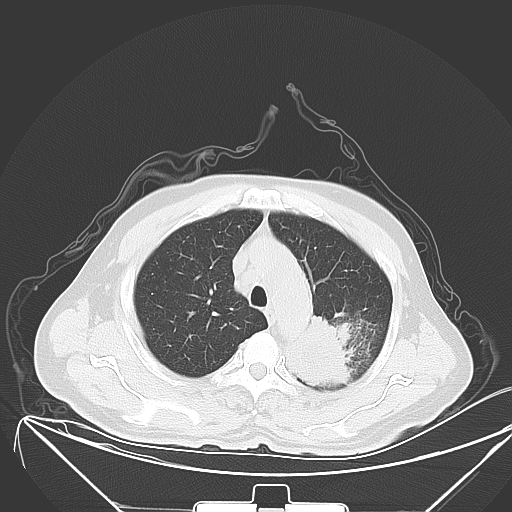
Chest CT, one axial slice; position 46 of 64 along the scan axis; 120 kVp; lung window (W 1500 / L -600 HU); 5 mm slice thickness; 512 × 512 image matrix. Patient: male, 58 years. From the clinical record (not read from this slice): clinical TNM (as recorded): T2b N3 M1b.
Structures marked on this image (bounding box drawn by a radiologist):
- lung tumour (recorded histology: adenocarcinoma): bounding box [x1, y1, x2, y2] px = [278, 308, 360, 394]